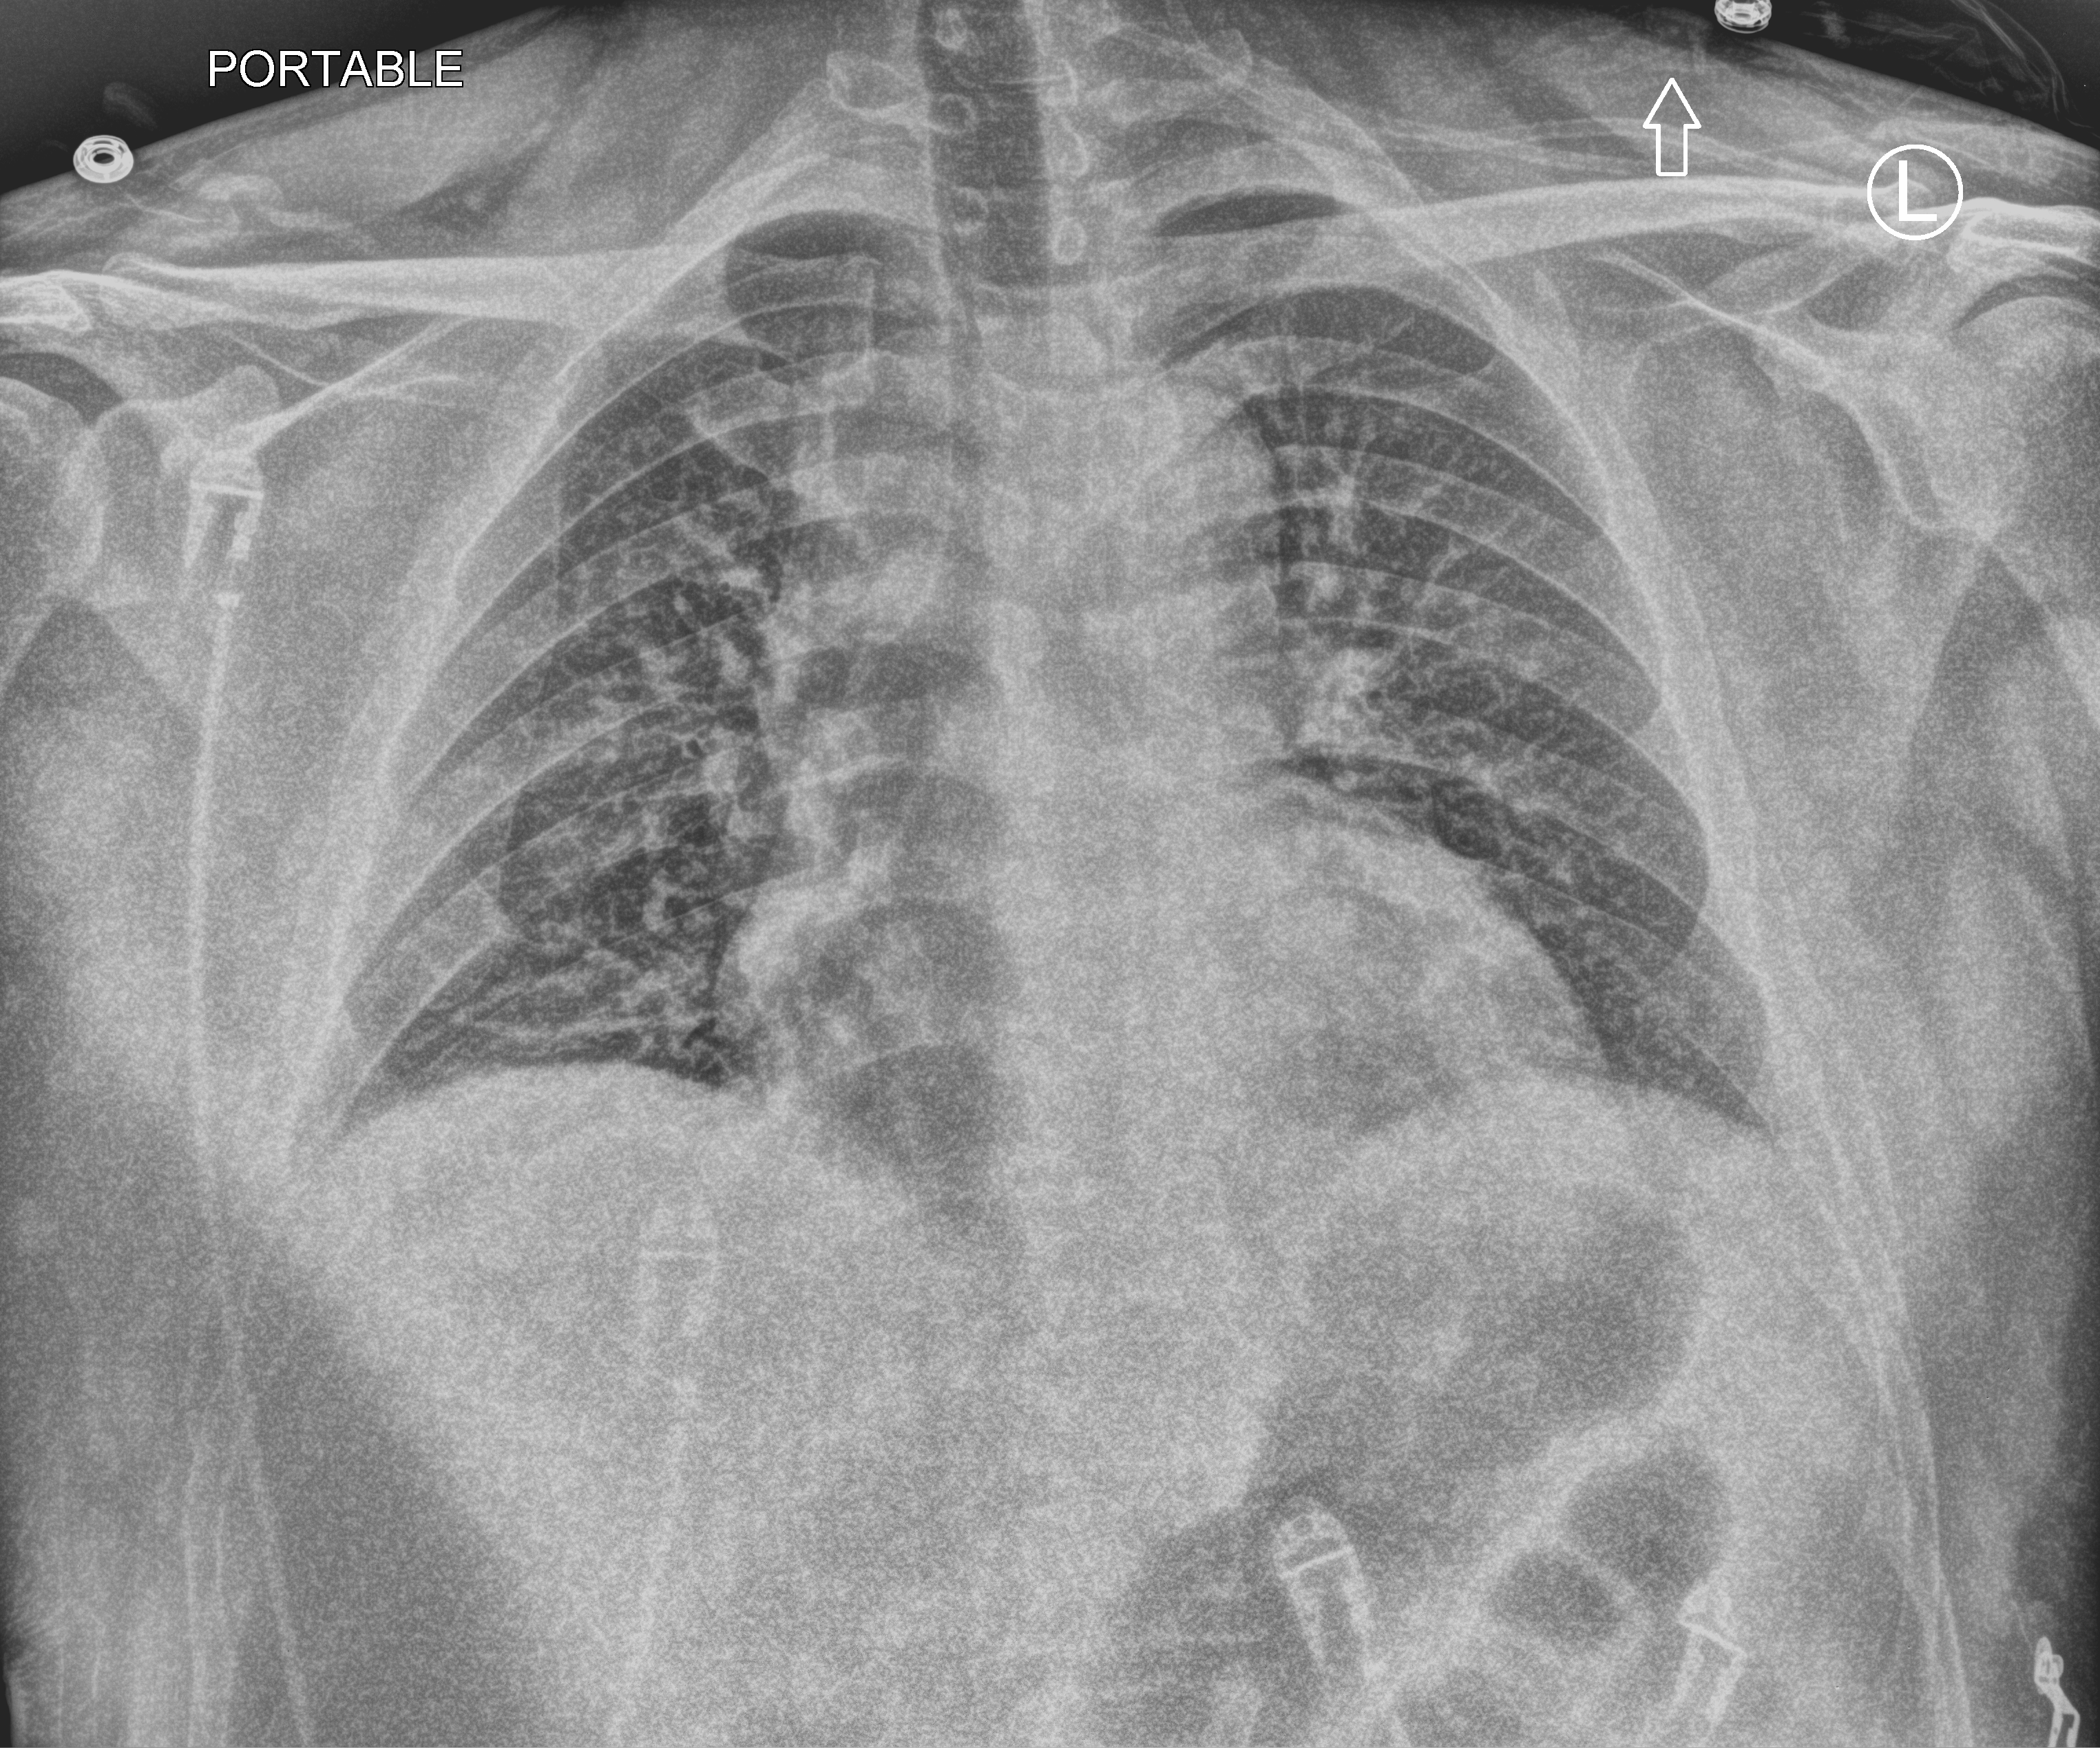
Portable chest radiograph; anteroposterior (AP) projection. Male patient hospitalised with COVID-19, age 18–59 years.
From the hospital-stay record, not from the radiograph (when in the stay this image was taken is not recorded):
- length of hospital stay: 6 days